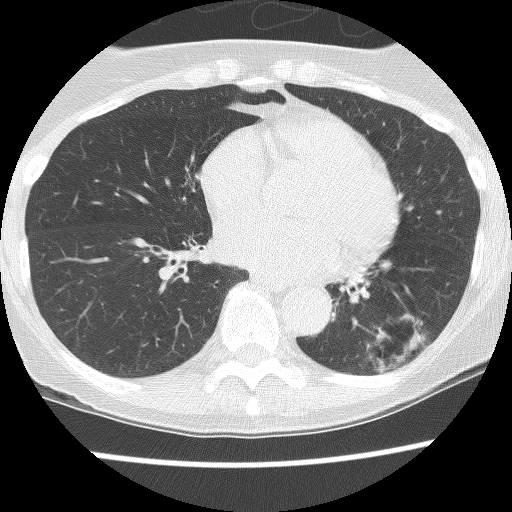
Low-dose screening chest CT, axial slice. Third screening round (two years after baseline). Lung window (W 1500 / L -600 HU). Slice 78 of 130 in the series. Female participant, aged 61 years at enrolment. Current smoker at enrolment.
Expert-annotated lung lesion, bounding box <329,289,452,392> (left, top, right, bottom; pixels). The screening reader recorded 2 non-calcified nodules or masses ≥4 mm on this exam (left lower lobe, left lower lobe); which of them this box marks is not recorded. Later outcome: lung cancer diagnosed 166 days after this screen — non-small cell carcinoma, left lower lobe, poorly differentiated (G3), stage IB (AJCC 6th edition), 100 mm at pathology.